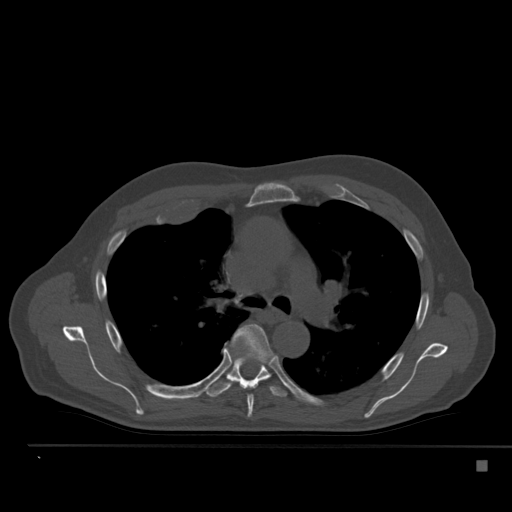
CT including the spine, one axial slice; reconstruction kernel Br40s; 120 kVp; bone window (W 1800 / L 400 HU); 512 × 512 image matrix. Male patient, age 70 years. From the clinical record (not read from this slice): primary cancer: renal.
Outlined on this slice (semi-automatically segmented with operator editing):
- T5 vertebra: box from (x=234, y=323) to (x=273, y=418) px
- T6 vertebra: (x=205, y=356)–(x=288, y=398)